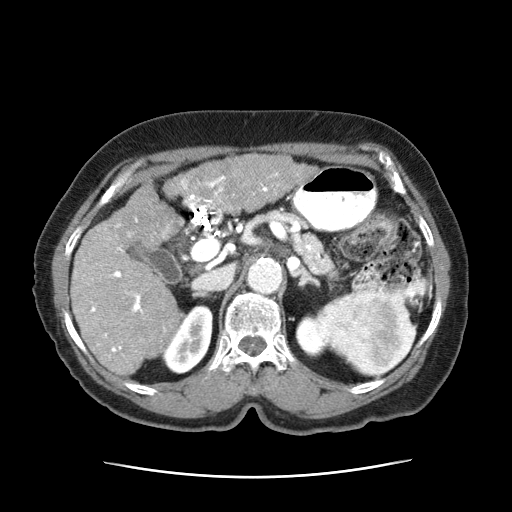
Contrast-enhanced abdominal CT (liver protocol), one axial slice. Slice 30 of 63 in the series (ordered by position). Reconstruction kernel STANDARD. 120 kVp. Soft-tissue window (W 400 / L 40 HU). 2.5 mm slice thickness. 512 × 512 image matrix. Female patient, age 79 years. From the clinical record (not read from this slice): diagnosis: hepatocellular carcinoma (patient treated with transarterial chemoembolisation; whether this scan precedes or follows treatment is not stated here); TNM stage (as recorded): Stage-II; Child-Pugh class: B.
Outlined on this slice (semi-automatically segmented with operator editing):
- abdominal aorta: box from (x=248, y=257) to (x=281, y=293) px
- liver parenchyma outside the tumour (the mass and vessels are separate outlines, so this box may not span the whole liver): (x=71, y=178)–(x=186, y=380)
- mass: (x=165, y=153)–(x=317, y=212)
- liver vessels: (x=90, y=175)–(x=226, y=358)